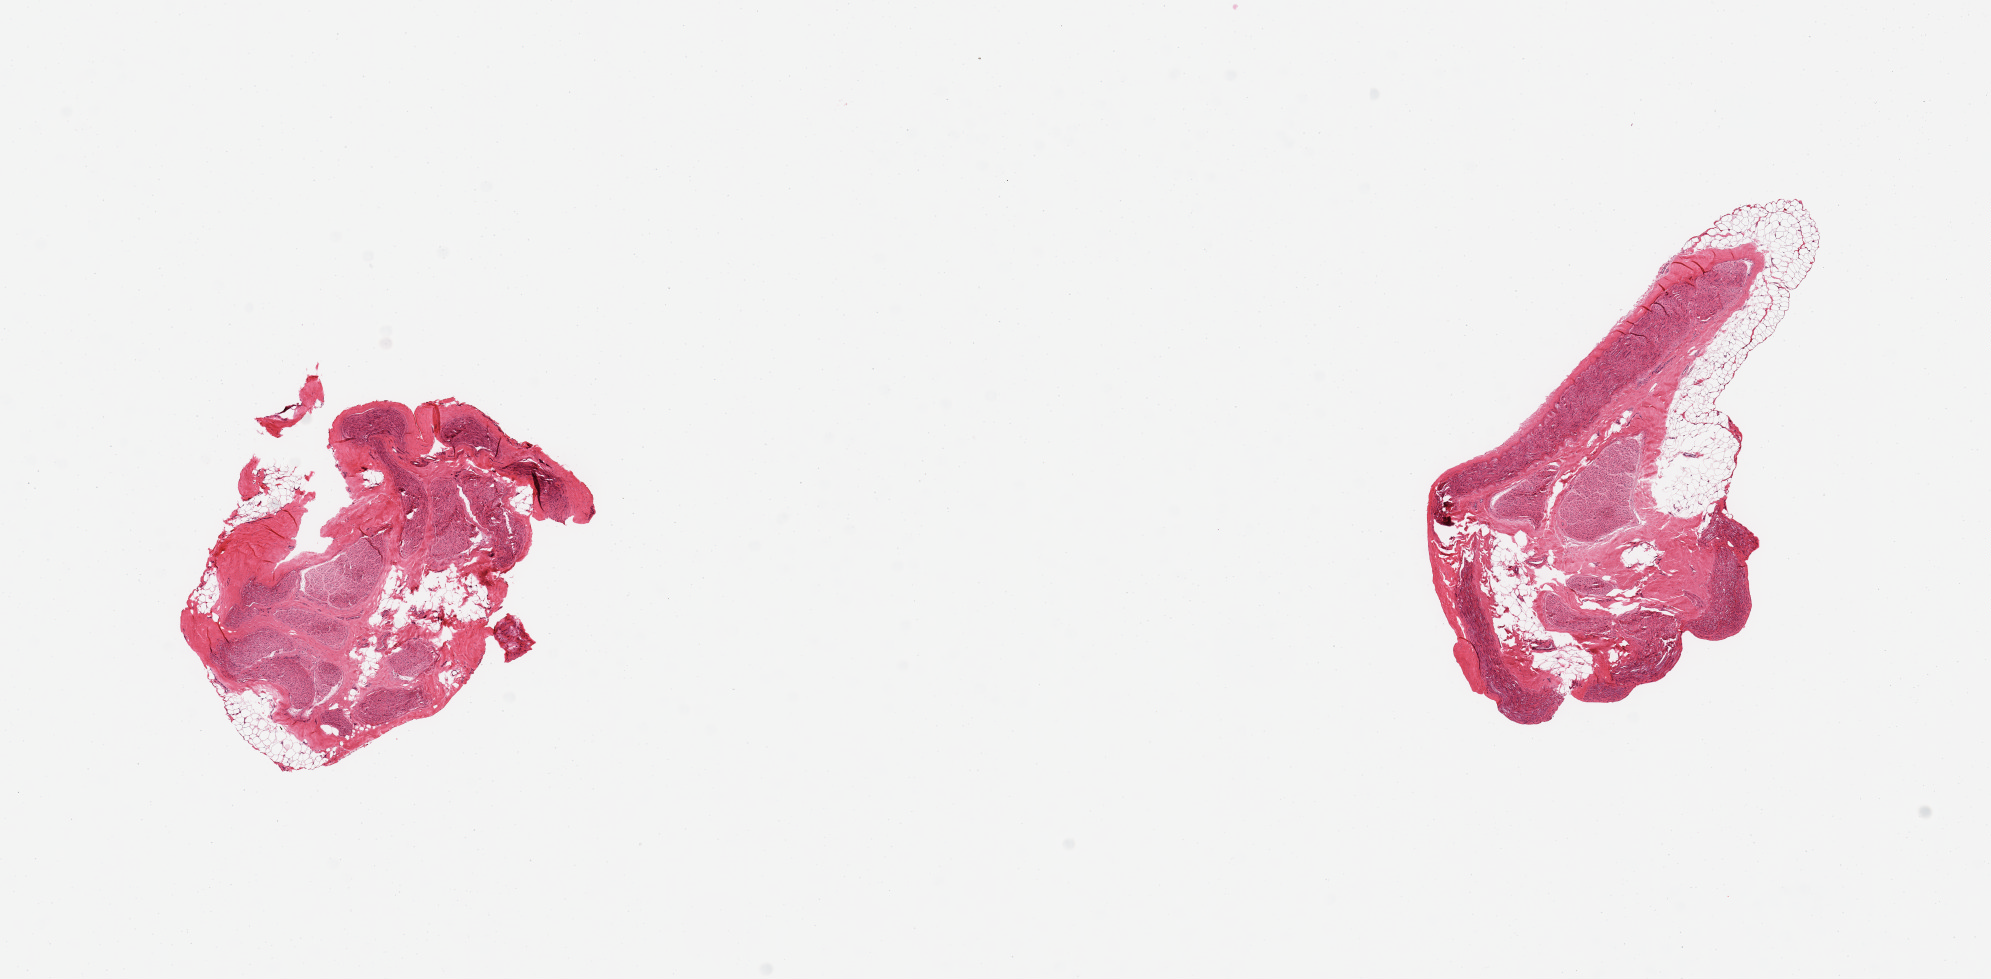
Hematoxylin and eosin (H&E) whole-slide image, low-resolution overview of the scanned area, about 15.8 x 7.7 mm (acquisition: 20x scan), PAXgene-fixed, paraffin-embedded tissue, target tissue: tibial nerve, tissue donor sample. Male donor.
Pathologist's review note for this sample: 2 pieces; ~20% to 30% internal/external fat.